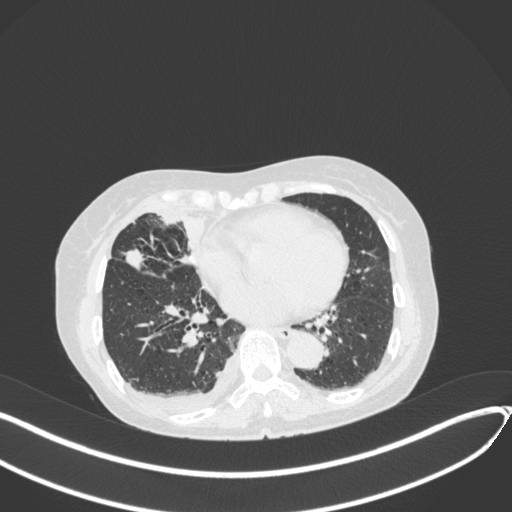
Chest CT, one axial slice. Reconstruction kernel B31f. Lung window (W 1500 / L -600 HU). 1 mm slice thickness. 512 × 512 image matrix, field of view 400 × 400 mm. Patient: female, 75 years. Case-level facts recorded for this patient, not image findings: clinical TNM (as recorded): T2a N3 M0.
Outlined on this slice (rectangle marked by the reading radiologist):
- lung tumour (recorded histology: adenocarcinoma): bounding box [x1, y1, x2, y2] px = [123, 246, 151, 274]